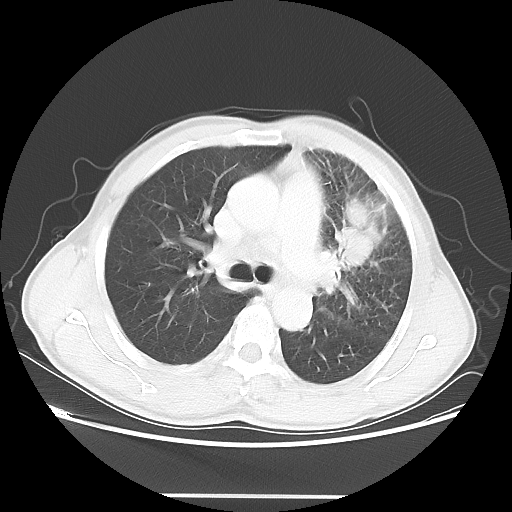
Chest CT, one axial slice. Slice 34 of 55 in the series (ordered by position). Reconstruction kernel LUNG. 100 kVp. Lung window (W 1500 / L -600 HU). 512 × 512 image matrix, field of view 398 × 398 mm. Male patient, age 60 years. From the clinical record (not read from this slice): clinical TNM (as recorded): T3 N3 M0.
Annotated regions visible in this slice (bounding box drawn by a radiologist):
- lung tumour (recorded histology: adenocarcinoma): bounding box [x1, y1, x2, y2] px = [336, 186, 381, 278]